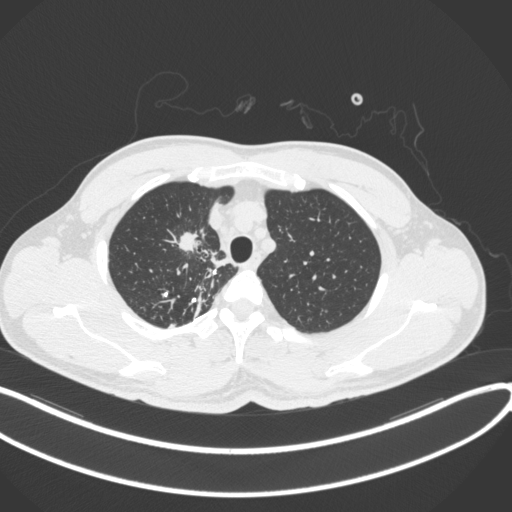
Chest CT, one axial slice. Slice 306 of 391 in the series (ordered by position). 120 kVp. Lung window (W 1500 / L -600 HU). 512 × 512 image matrix. Male patient, age 48 years. From the clinical record (not read from this slice): clinical TNM (as recorded): T1c N1 M1.
Outlined on this slice (rectangle marked by the reading radiologist):
- lung tumour (recorded histology: adenocarcinoma): bounding box (x1, y1, x2, y2) in pixels: (170, 226, 208, 255)